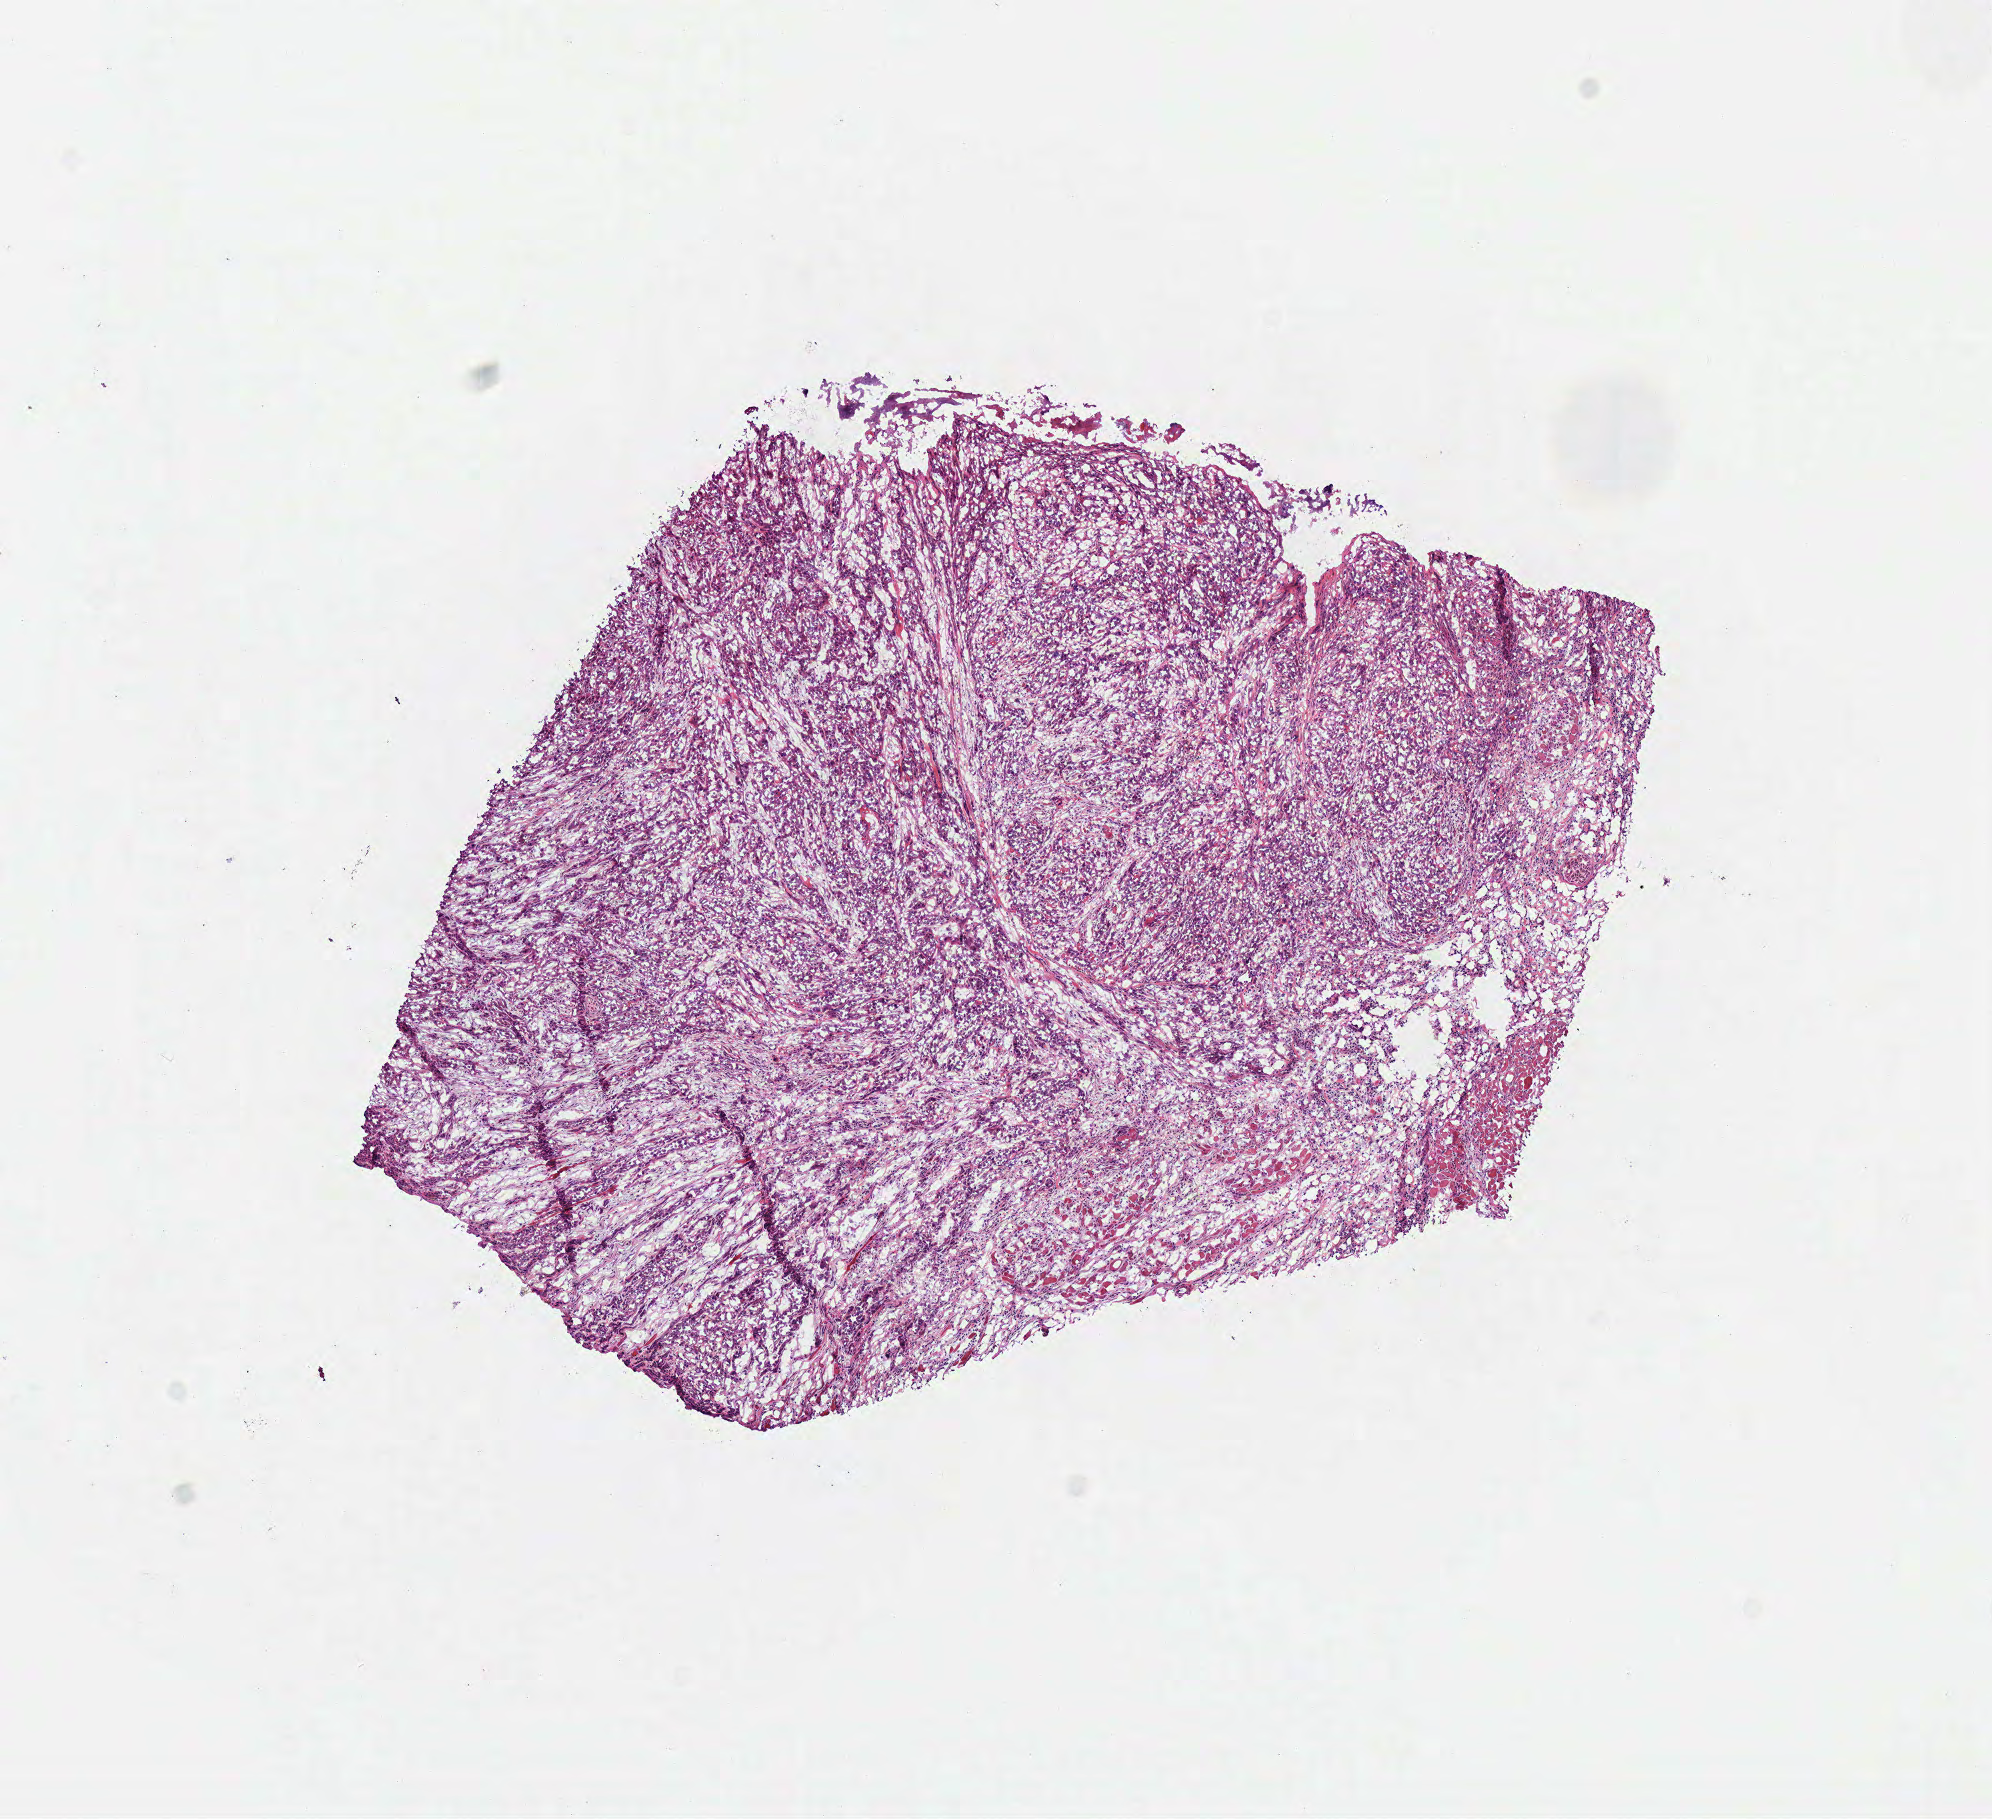
Digitized H&E tissue section (whole slide) — low-resolution overview of the scanned area, about 7.8 x 7.2 mm. Frozen section from the bottom of the tissue portion. Head and neck, primary tumour sample. Female, age 76 years at initial diagnosis. Histologic grade: G3 (poorly differentiated). Slide review estimates, as recorded: tumour cells 85%, tumour nuclei 70%, normal cells 5%, stromal cells 10%, necrosis 0%.
* lymph nodes positive (case pathology): 3 of 24 examined
* AJCC pathologic stage: IVA (7th edition)
* diagnosis: Squamous cell carcinoma, NOS